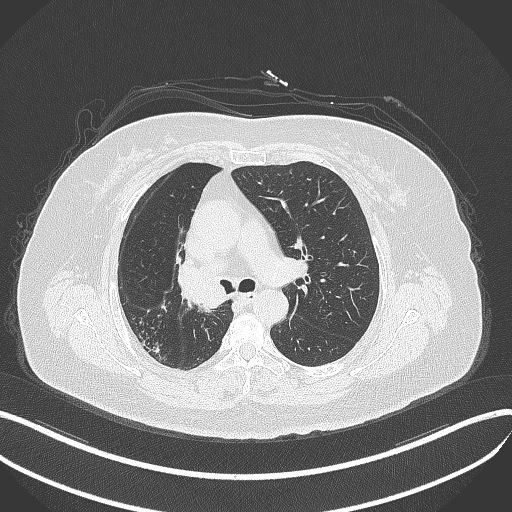
Chest CT, one axial slice; 120 kVp; lung window (W 1500 / L -600 HU); 1 mm slice thickness; 512 × 512 image matrix, field of view 400 × 400 mm. Patient: female, 60 years. Case-level facts recorded for this patient, not image findings: clinical TNM (as recorded): T1c N0 M0.
Outlined on this slice (bounding box drawn by a radiologist):
- lung tumour (recorded histology: squamous cell carcinoma): bounding box [x1, y1, x2, y2] px = [173, 257, 232, 311]